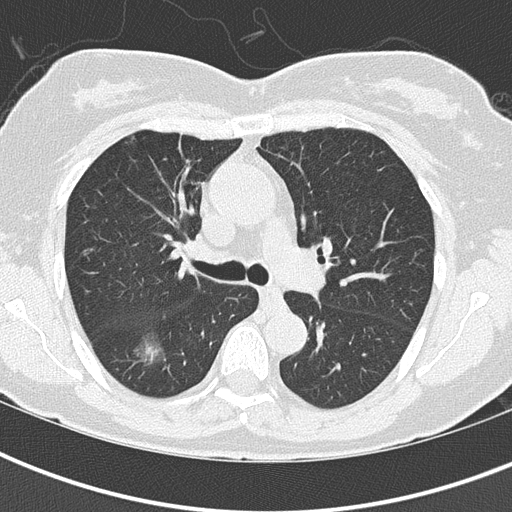
Low-dose screening chest CT, axial slice, first (baseline) screen, lung window (W 1500 / L -600 HU), 2 mm slice thickness, 512 × 512 image matrix. Female, age 68 years at enrolment. Former smoker at enrolment.
Expert-annotated lung lesion, bounding box (x1, y1, x2, y2) in pixels: (120, 326, 178, 377). Reader record for this screening exam (exam-level; its link to the box is not recorded): non-calcified nodule or mass ≥4 mm, right lower lobe, 19 × 17 mm, spiculated (stellate) margins, ground glass attenuation. Official screen result: positive, change unspecified: nodule(s) >= 4 mm or enlarging nodule(s), mass(es), or other non-specific abnormalities suspicious for lung cancer.